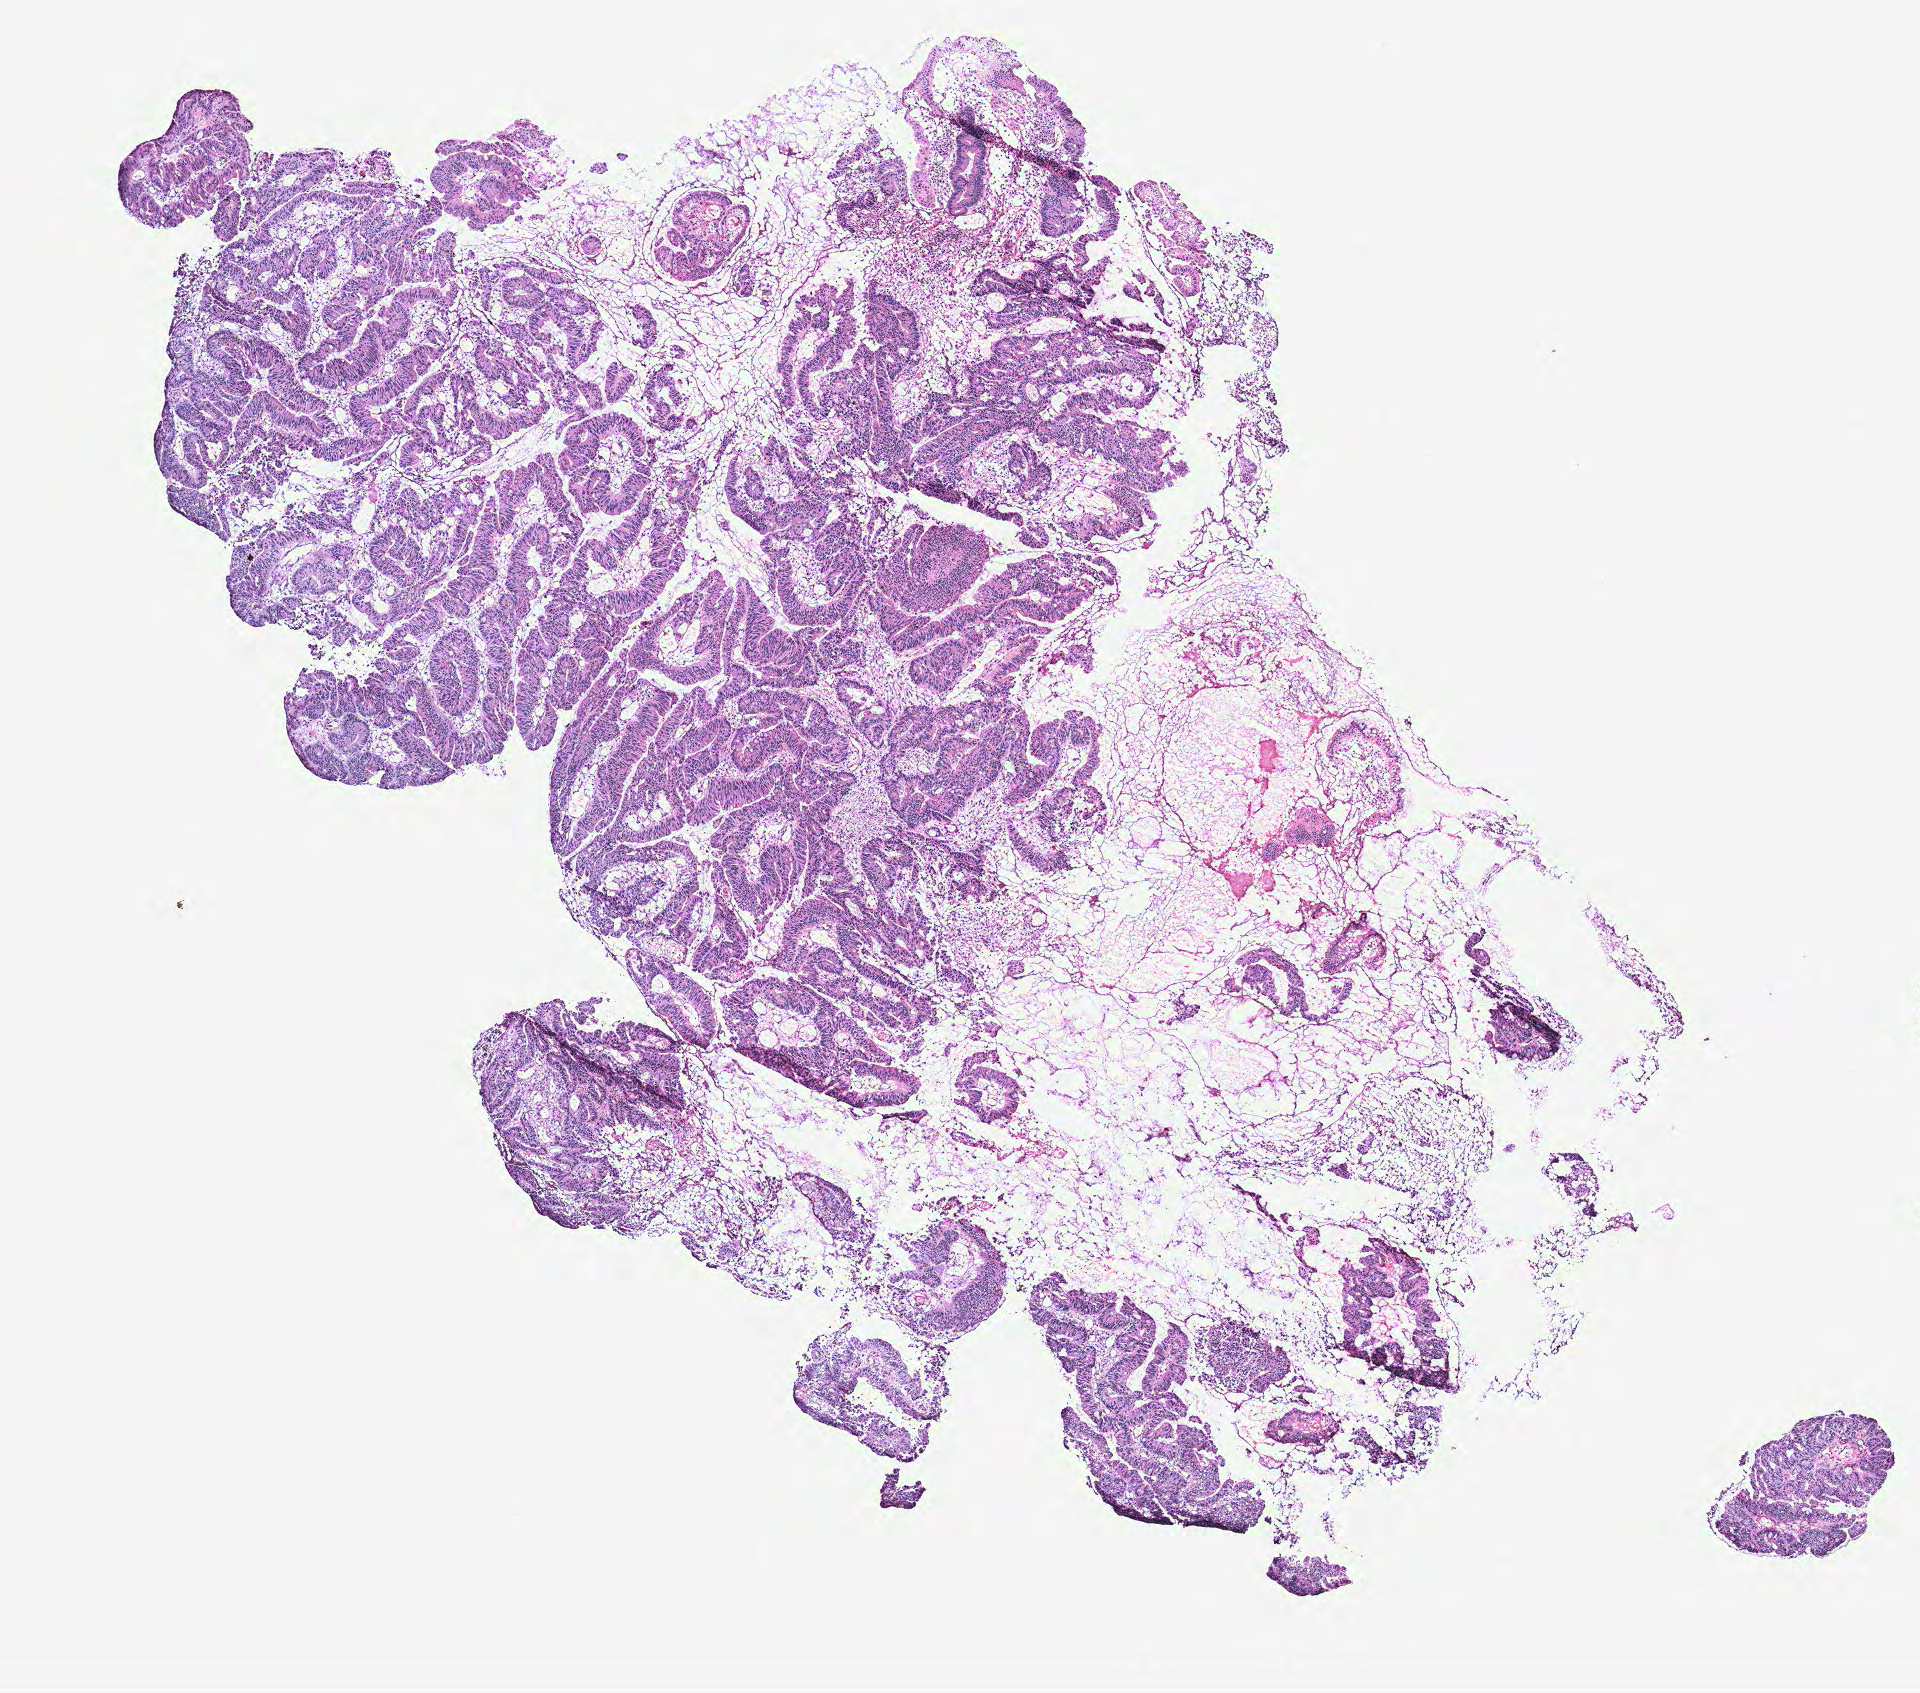
Whole-slide histology image, H&E — a low-resolution overview of the entire scanned area, about 7.7 x 6.8 mm (from a 40x scan); colon, normal (non-tumour) tissue. Male, 51 y/o.
* this section: normal (non-tumour) tissue from the same patient
* patient diagnosis: Adenocarcinoma, NOS